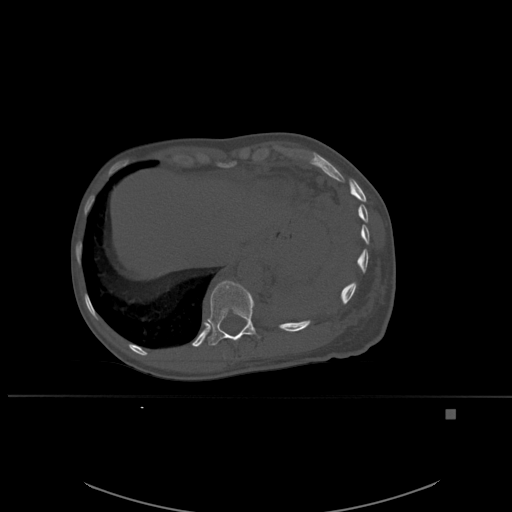
CT including the spine, one axial slice; bone window (W 1800 / L 400 HU); 1.5 mm slice thickness; 512 × 512 image matrix, field of view 440 × 440 mm. Female patient, age 45 years. From the clinical record (not read from this slice): primary cancer: lung.
Outlined on this slice (semi-automatic segmentation, software-assisted and operator-edited):
- T11 vertebra: box from (x=207, y=280) to (x=260, y=346) px